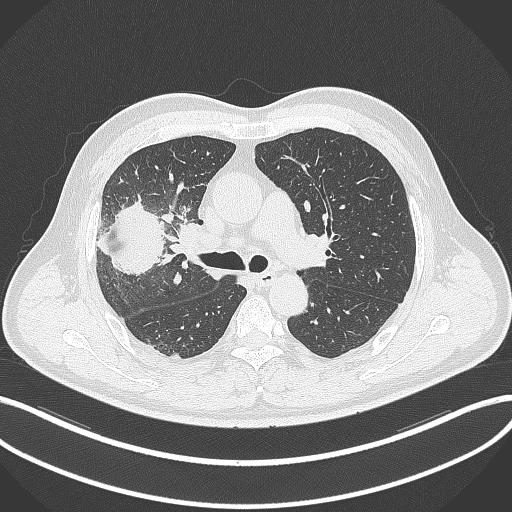
Chest CT, one axial slice. Slice 209 of 348 in the series (ordered by position). Reconstruction kernel B70f. 120 kVp. Lung window (W 1500 / L -600 HU). 1 mm slice thickness. 512 × 512 image matrix, field of view 400 × 400 mm. Male patient, age 55 years. From the clinical record (not read from this slice): clinical TNM (as recorded): T3 N2 M1.
Outlined on this slice (bounding box drawn by a radiologist):
- lung tumour (recorded histology: adenocarcinoma): bounding box <94,193,165,278> (left, top, right, bottom; pixels)